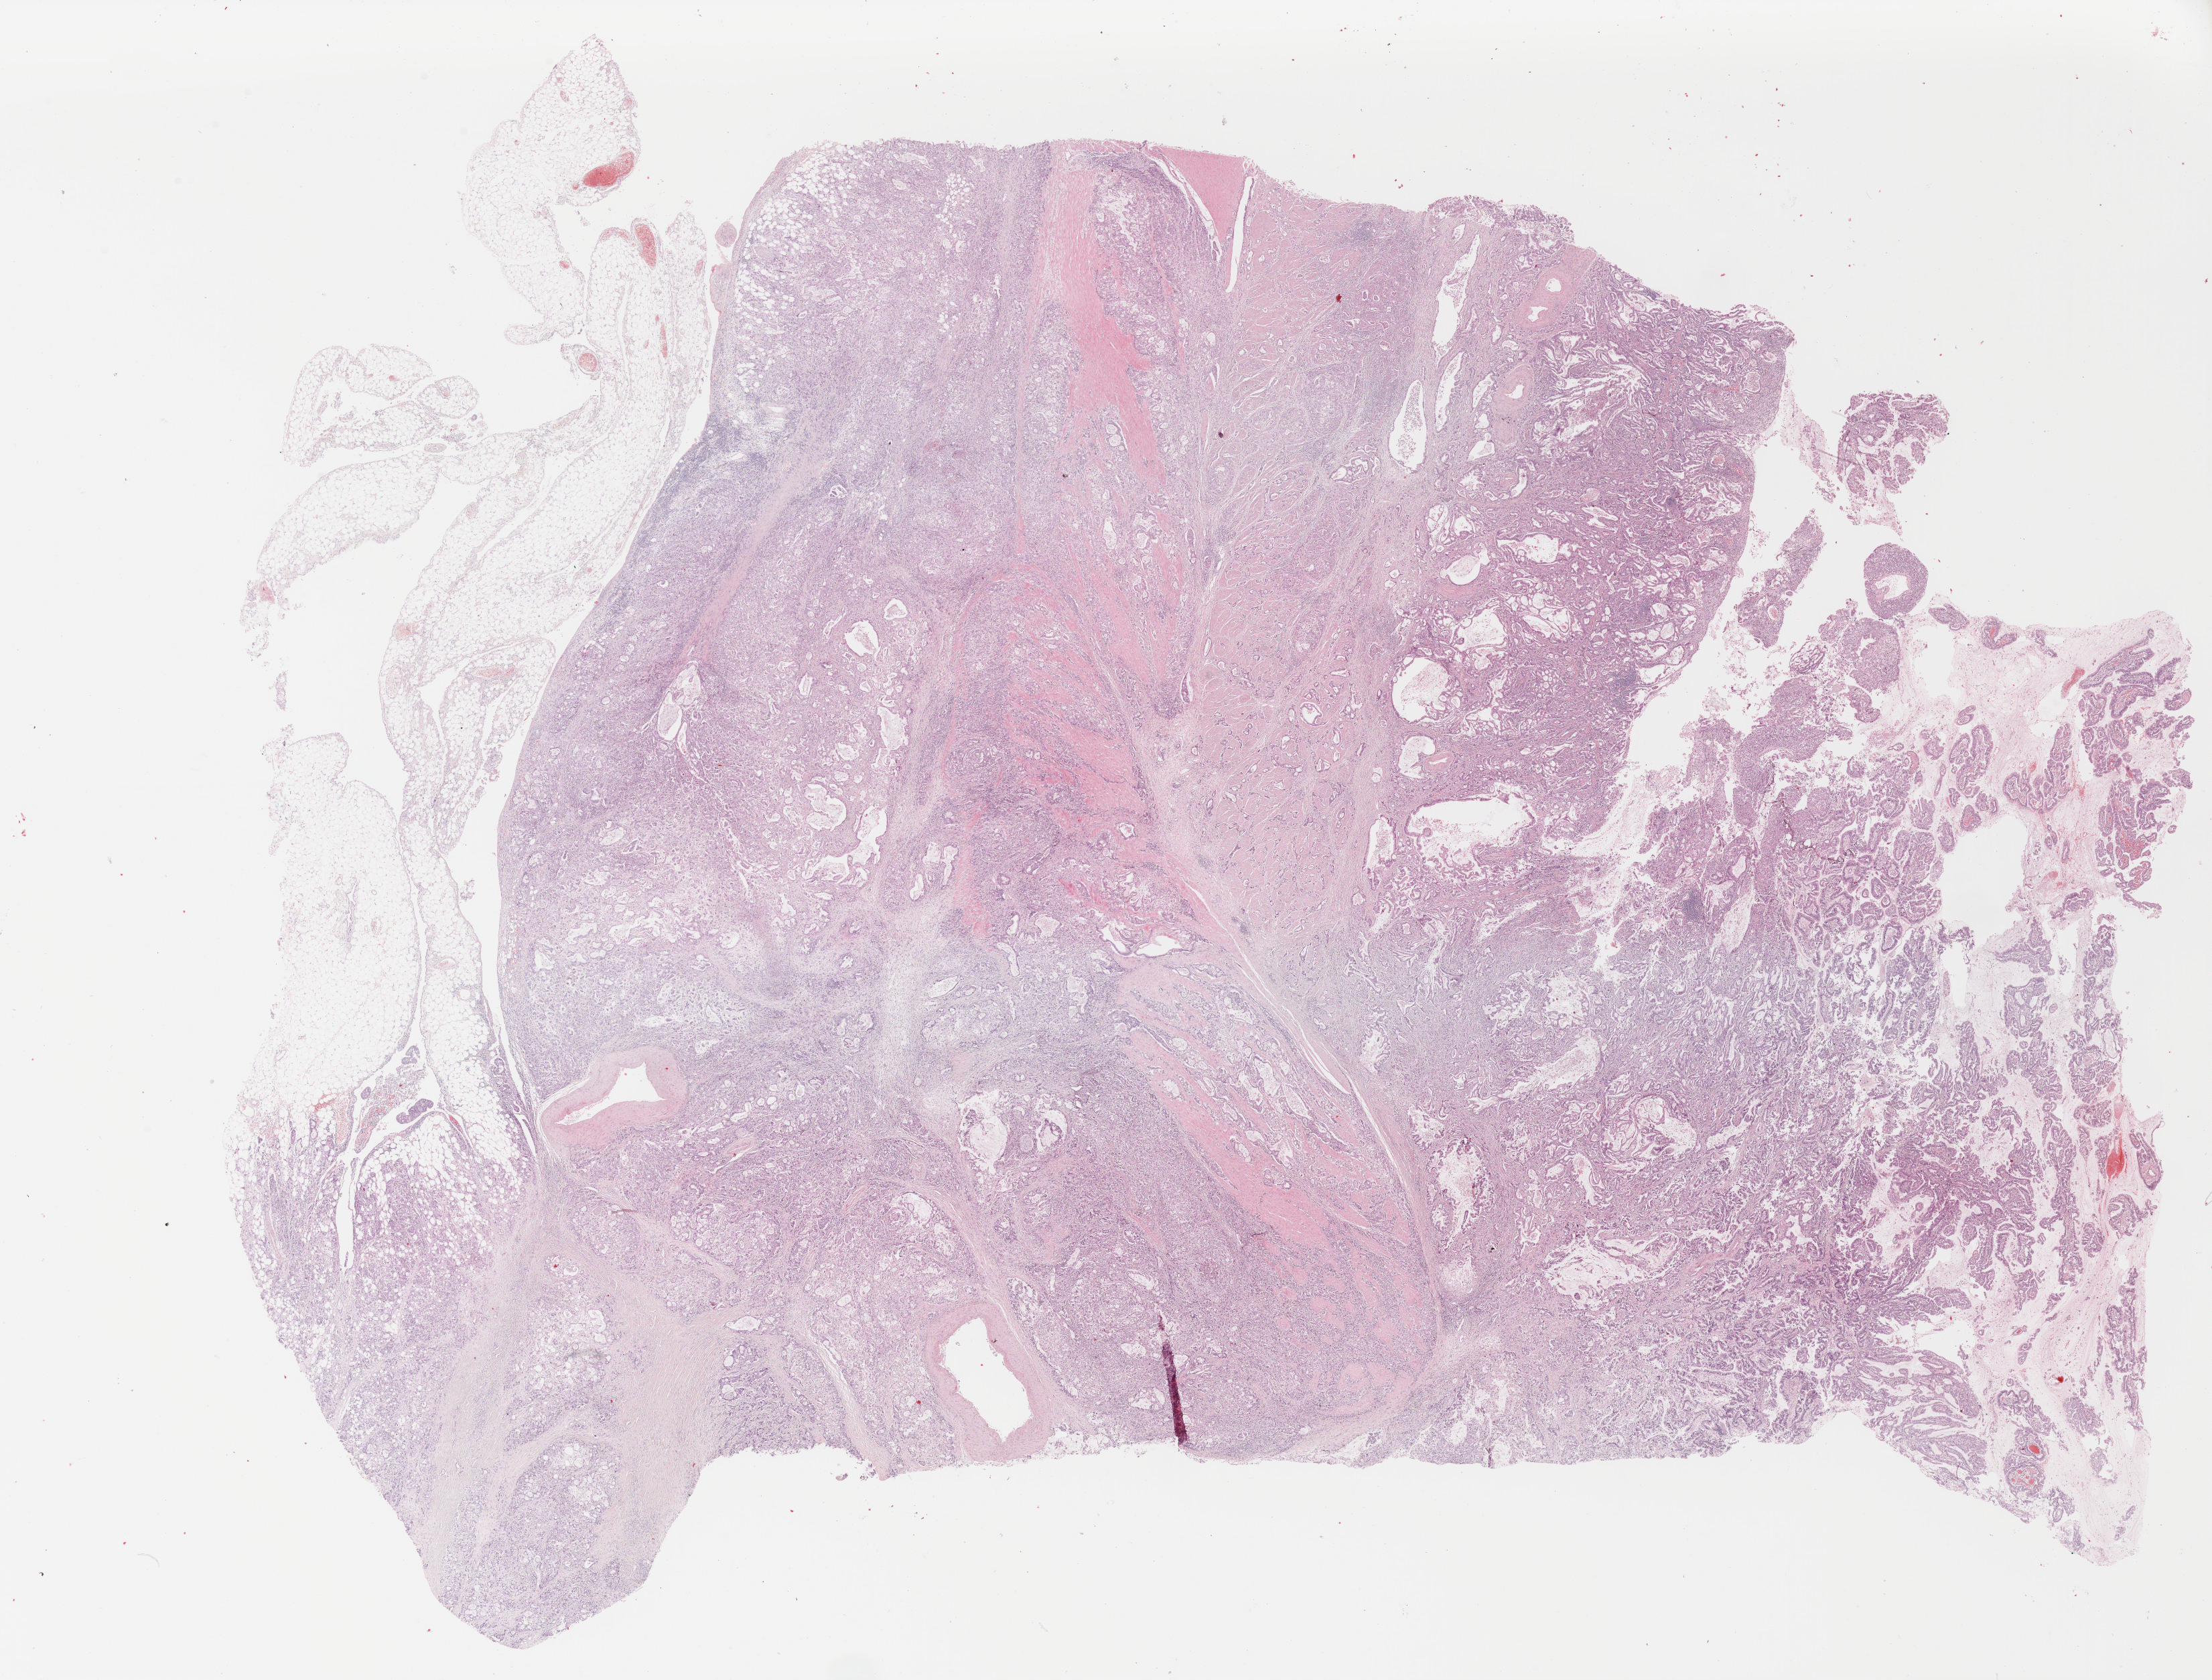
H&E-stained whole-slide image, shown as a low-resolution overview of the whole scanned area (about 26.0 x 19.8 mm), formalin-fixed paraffin-embedded (FFPE) diagnostic section, sample: primary tumour, stomach. Male patient; age at initial diagnosis 75 years. Histologic grade: G3 (poorly differentiated).
Lymph nodes positive (case pathology): 6 of 15 examined. TNM: T3 N2 M0. Histologic diagnosis: Tubular adenocarcinoma (fundus of stomach). AJCC pathologic stage: IIIA (7th edition).